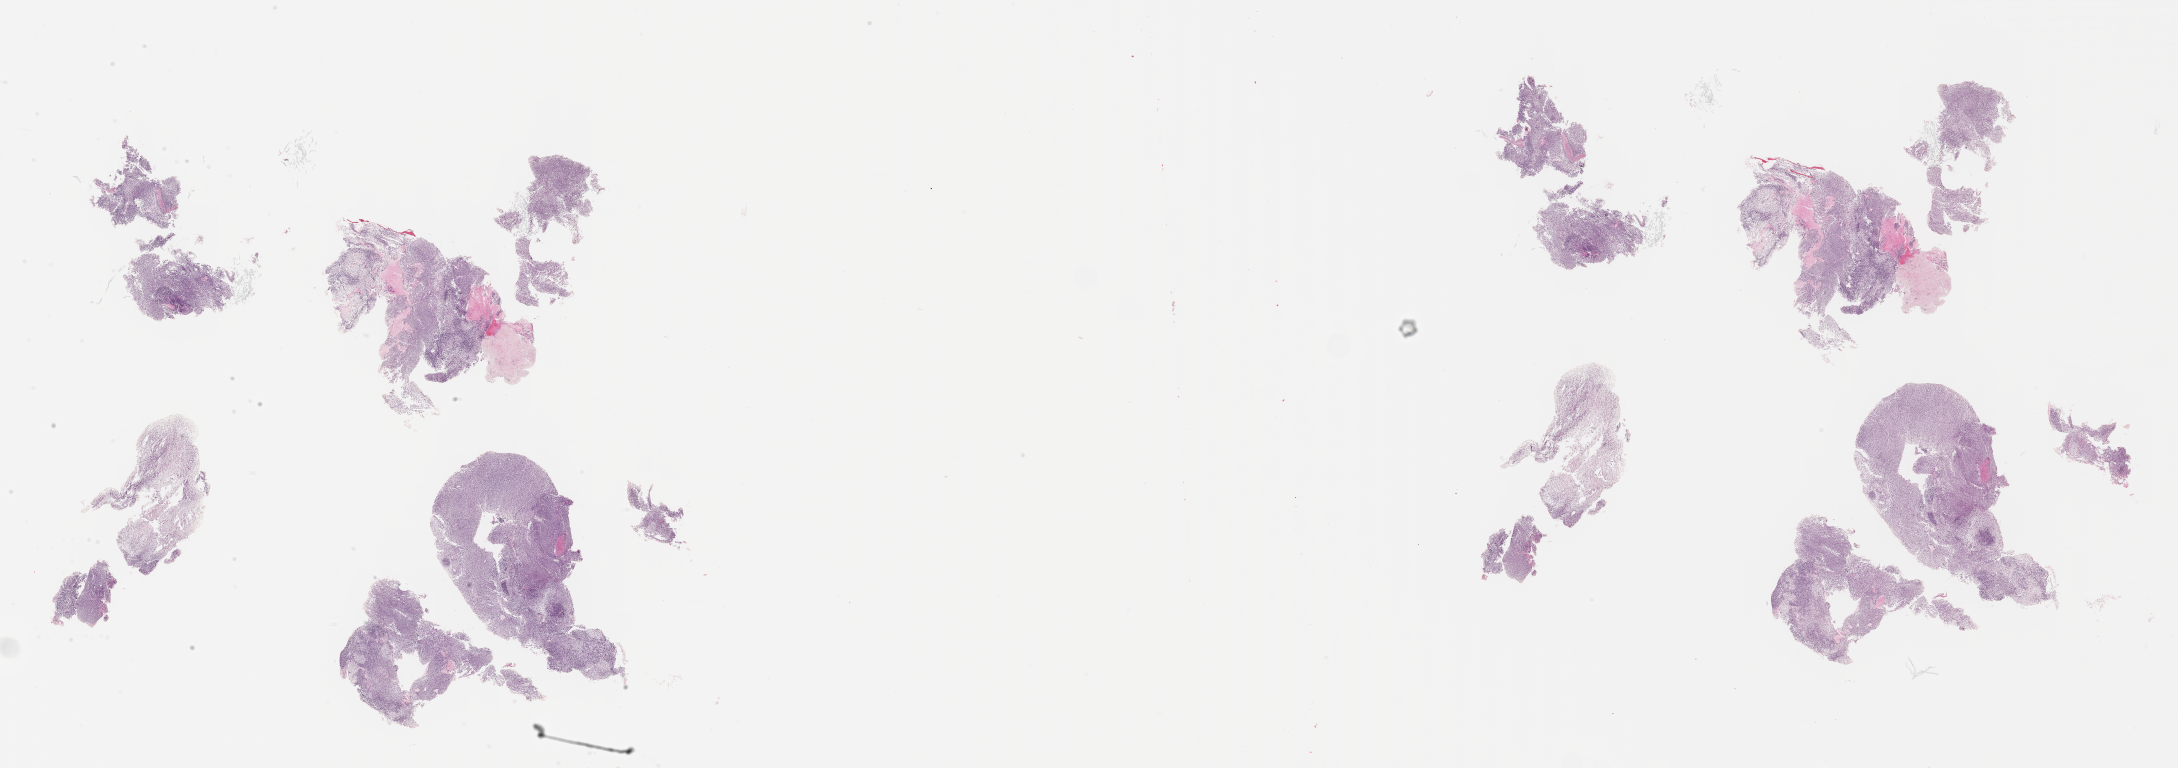
Digitized H&E-stained section of tumor tissue, whole scanned area (about 35.2 x 12.4 mm) shown as a low-resolution overview; FFPE section; sample anatomic site: neck-right. Female patient, age at diagnosis 8.4 years.
Stage (as recorded): 3. Diagnosis: rhabdomyosarcoma; histological classification: embryonal rhabdomyosarcoma. Metastatic status at presentation (as recorded): non-metastatic. Primary site (case record): infratemporal Fossa.